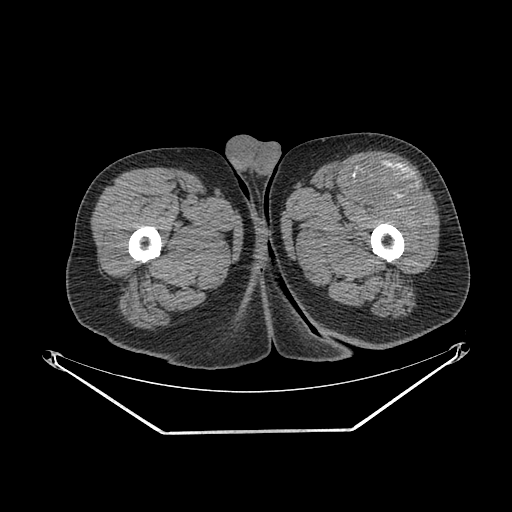
CT of an extremity soft-tissue mass (from a PET/CT study), one axial slice; soft-tissue window (W 400 / L 40 HU); 512 × 512 image matrix. Male patient. Case-level facts recorded for this patient, not image findings: histological type: extraskeletal osteosarcoma; grade: high; site of the primary tumour: thigh.
Annotated regions visible in this slice (expert contour drawn on MRI and transferred to this co-registered scan by the dataset authors):
- gross tumour volume (mass): bounding box <361,169,419,202> (left, top, right, bottom; pixels)